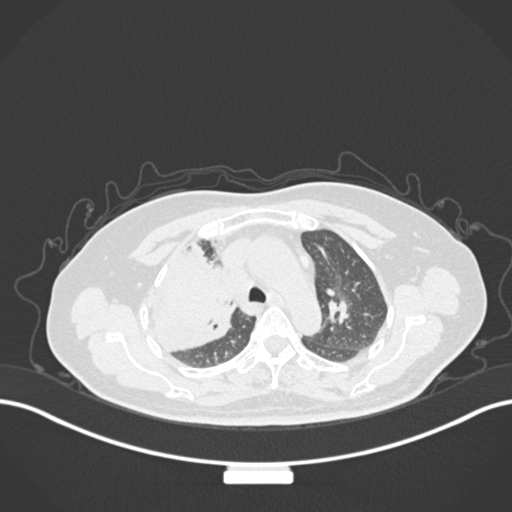
Chest CT, one axial slice; position 112 of 177 along the scan axis; reconstruction kernel B30f; lung window (W 1500 / L -600 HU); 1 mm slice thickness; 512 × 512 image matrix, field of view 400 × 400 mm. Patient: female, 60 years. From the clinical record (not read from this slice): clinical TNM (as recorded): T3 N1 M1.
Structures marked on this image (rectangle marked by the reading radiologist):
- lung tumour (recorded histology: adenocarcinoma): box from (x=148, y=247) to (x=243, y=363) px